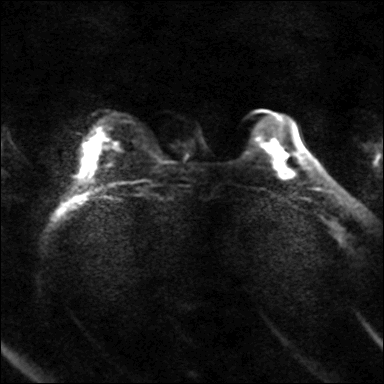
Breast MRI, one axial slice. Position 12 of 40 along the scan axis. Diffusion-weighted series; image 2 of 4 stored at this slice position (different b-values; order by instance number). 3 T. 4 mm slice thickness. 384 × 384 image matrix. Female patient.
Annotated regions visible in this slice (outlined manually by an expert reader):
- tumour on diffusion-weighted imaging: bounding box [x1, y1, x2, y2] px = [281, 154, 286, 160]